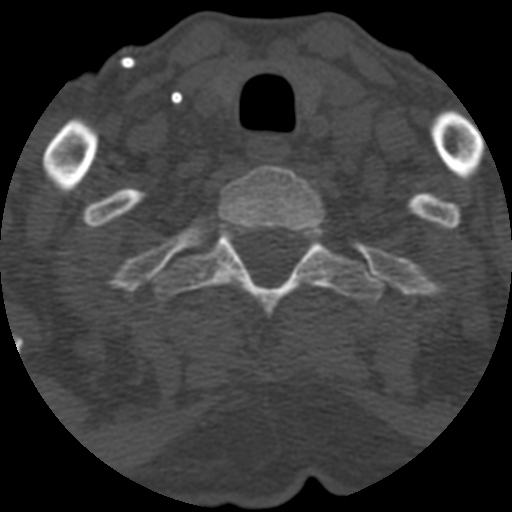
CT including the spine, one axial slice; slice 510 of 708 in the series (ordered by position); reconstruction kernel STANDARD; one of 3 acquisitions stored at this slice position; bone window (W 1800 / L 400 HU); 512 × 512 image matrix. Patient age 55 years. Case-level facts recorded for this patient, not image findings: primary cancer: colon; vertebrae with lytic lesions (as recorded): T12, L1, L5.
Annotated regions visible in this slice (semi-automatically segmented with operator editing):
- T1 vertebra: bounding box [x1, y1, x2, y2] px = [219, 165, 324, 230]
- T2 vertebra: [151, 224, 385, 318]